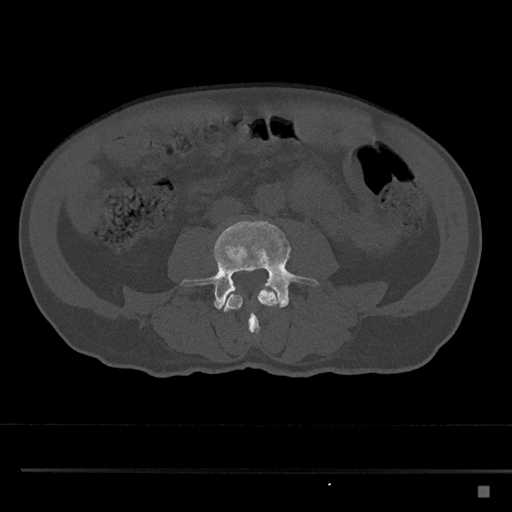
CT including the spine, one axial slice. Slice 657 of 797 in the series (ordered by position). Bone window (W 1800 / L 400 HU). 0.5 mm slice thickness. 512 × 512 image matrix, field of view 391 × 391 mm. Male patient, age 59 years. From the clinical record (not read from this slice): primary cancer: prostate.
Structures marked on this image (semi-automatic segmentation, software-assisted and operator-edited):
- L3 vertebra: bounding box (x1, y1, x2, y2) in pixels: (221, 282, 279, 334)
- L4 vertebra: (180, 219, 320, 309)